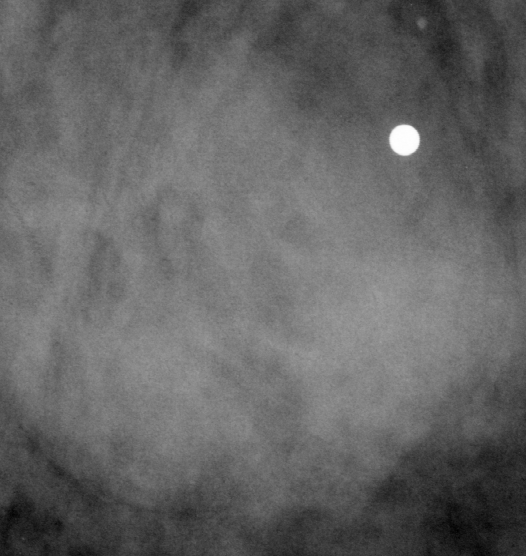
Region of interest cut from a scanned film mammogram (one marked finding), left breast, MLO view.
Mass, shape round, margins microlobulated; BI-RADS assessment category 3; pathology (as recorded): benign.